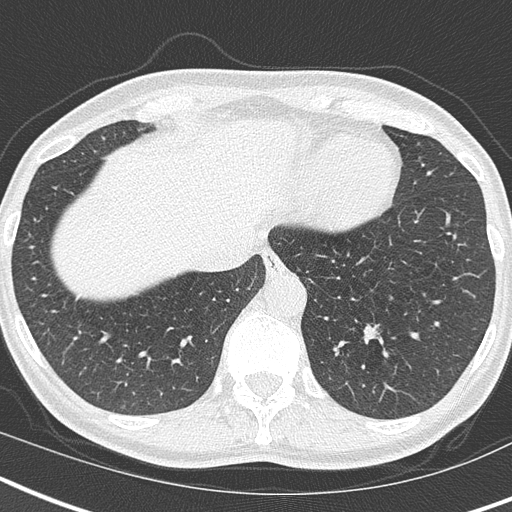
Axial slice from a low-dose chest CT screening exam, third annual screen, lung window (W 1500 / L -600 HU), 2 mm slice thickness, lung (sharp) reconstruction kernel (B50f), 512 × 512 image matrix, field of view 293 × 293 mm. Female participant, aged 55 years at enrolment. Current smoker at enrolment.
Expert-annotated lung lesion, box from (x=347, y=307) to (x=398, y=362) px. The screening reader recorded 2 non-calcified nodules or masses ≥4 mm on this exam (left lower lobe, right upper lobe); which of them this box marks is not recorded. Official screen result: positive, other.